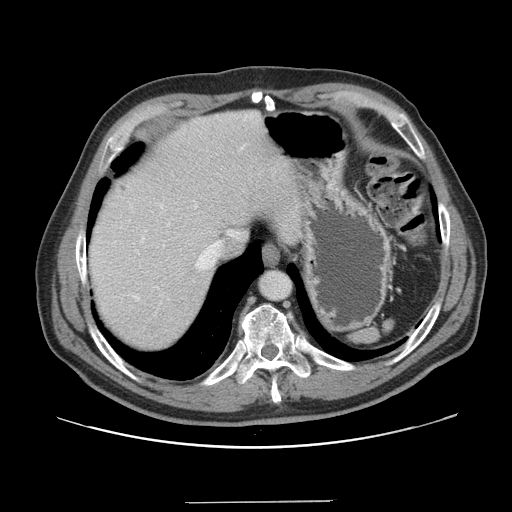
Contrast-enhanced abdominal CT, one axial slice. Slice 131 of 151 in the series (ordered by position). 120 kVp. Intravenous contrast given. Soft-tissue window (W 400 / L 40 HU). 2.5 mm slice thickness. 512 × 512 image matrix, field of view 399 × 399 mm. Male patient, age 63 years. Case-level facts recorded for this patient, not image findings: diagnosis: colorectal cancer liver metastases, imaged before liver resection; multiple liver metastases: no; largest metastasis: 2.1 cm; disease in both lobes: no.
Annotated regions visible in this slice (expert manual segmentation):
- hepatic veins: bounding box <143,238,220,269> (left, top, right, bottom; pixels)
- liver: <89,111,305,352>
- planned liver remnant (the part of the liver to remain after resection): <89,125,246,352>